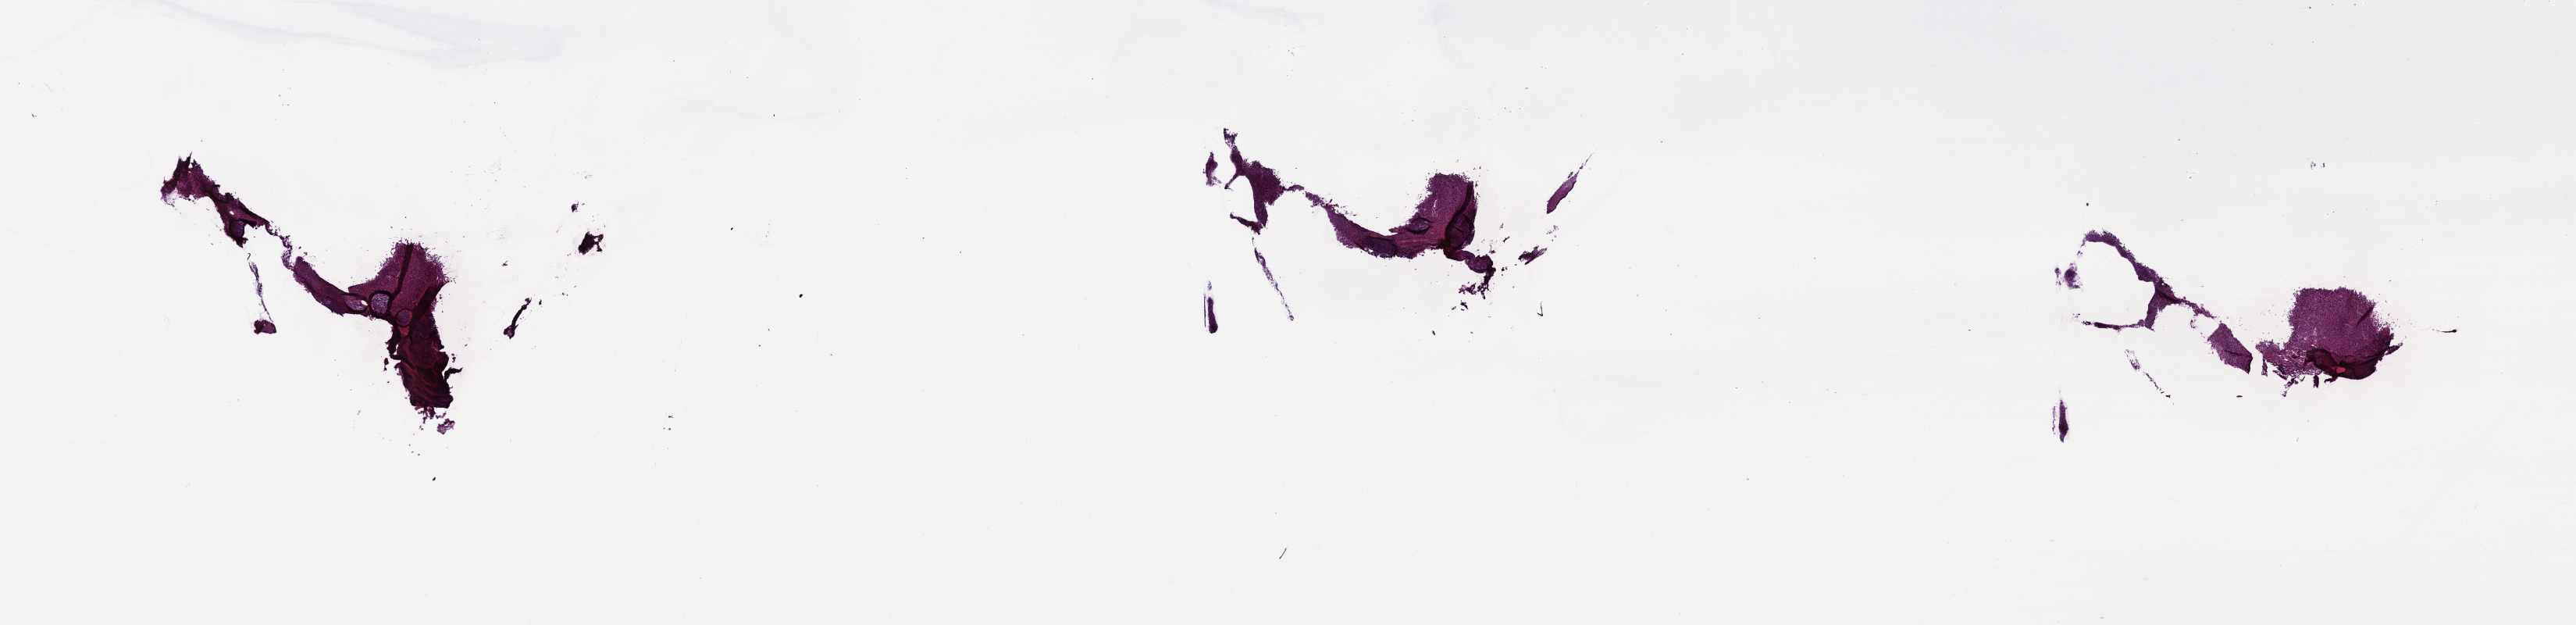
H&E-stained whole-slide image — a low-resolution overview of the entire scanned area, about 26.7 x 6.5 mm, frozen section from the top of the tissue portion, brain, primary tumour sample. Patient: male, age at initial diagnosis 44 years. Histologic grade: G3 (poorly differentiated). Composition of this section per pathologist review: tumour cells 50%, tumour nuclei 80%, normal cells 5%, stromal cells 45%, necrosis 0%. Inflammatory infiltration, as recorded: lymphocyte infiltration 0%, monocyte infiltration 0%, neutrophil infiltration 0%.
- pathologic diagnosis: Mixed glioma (cerebrum)